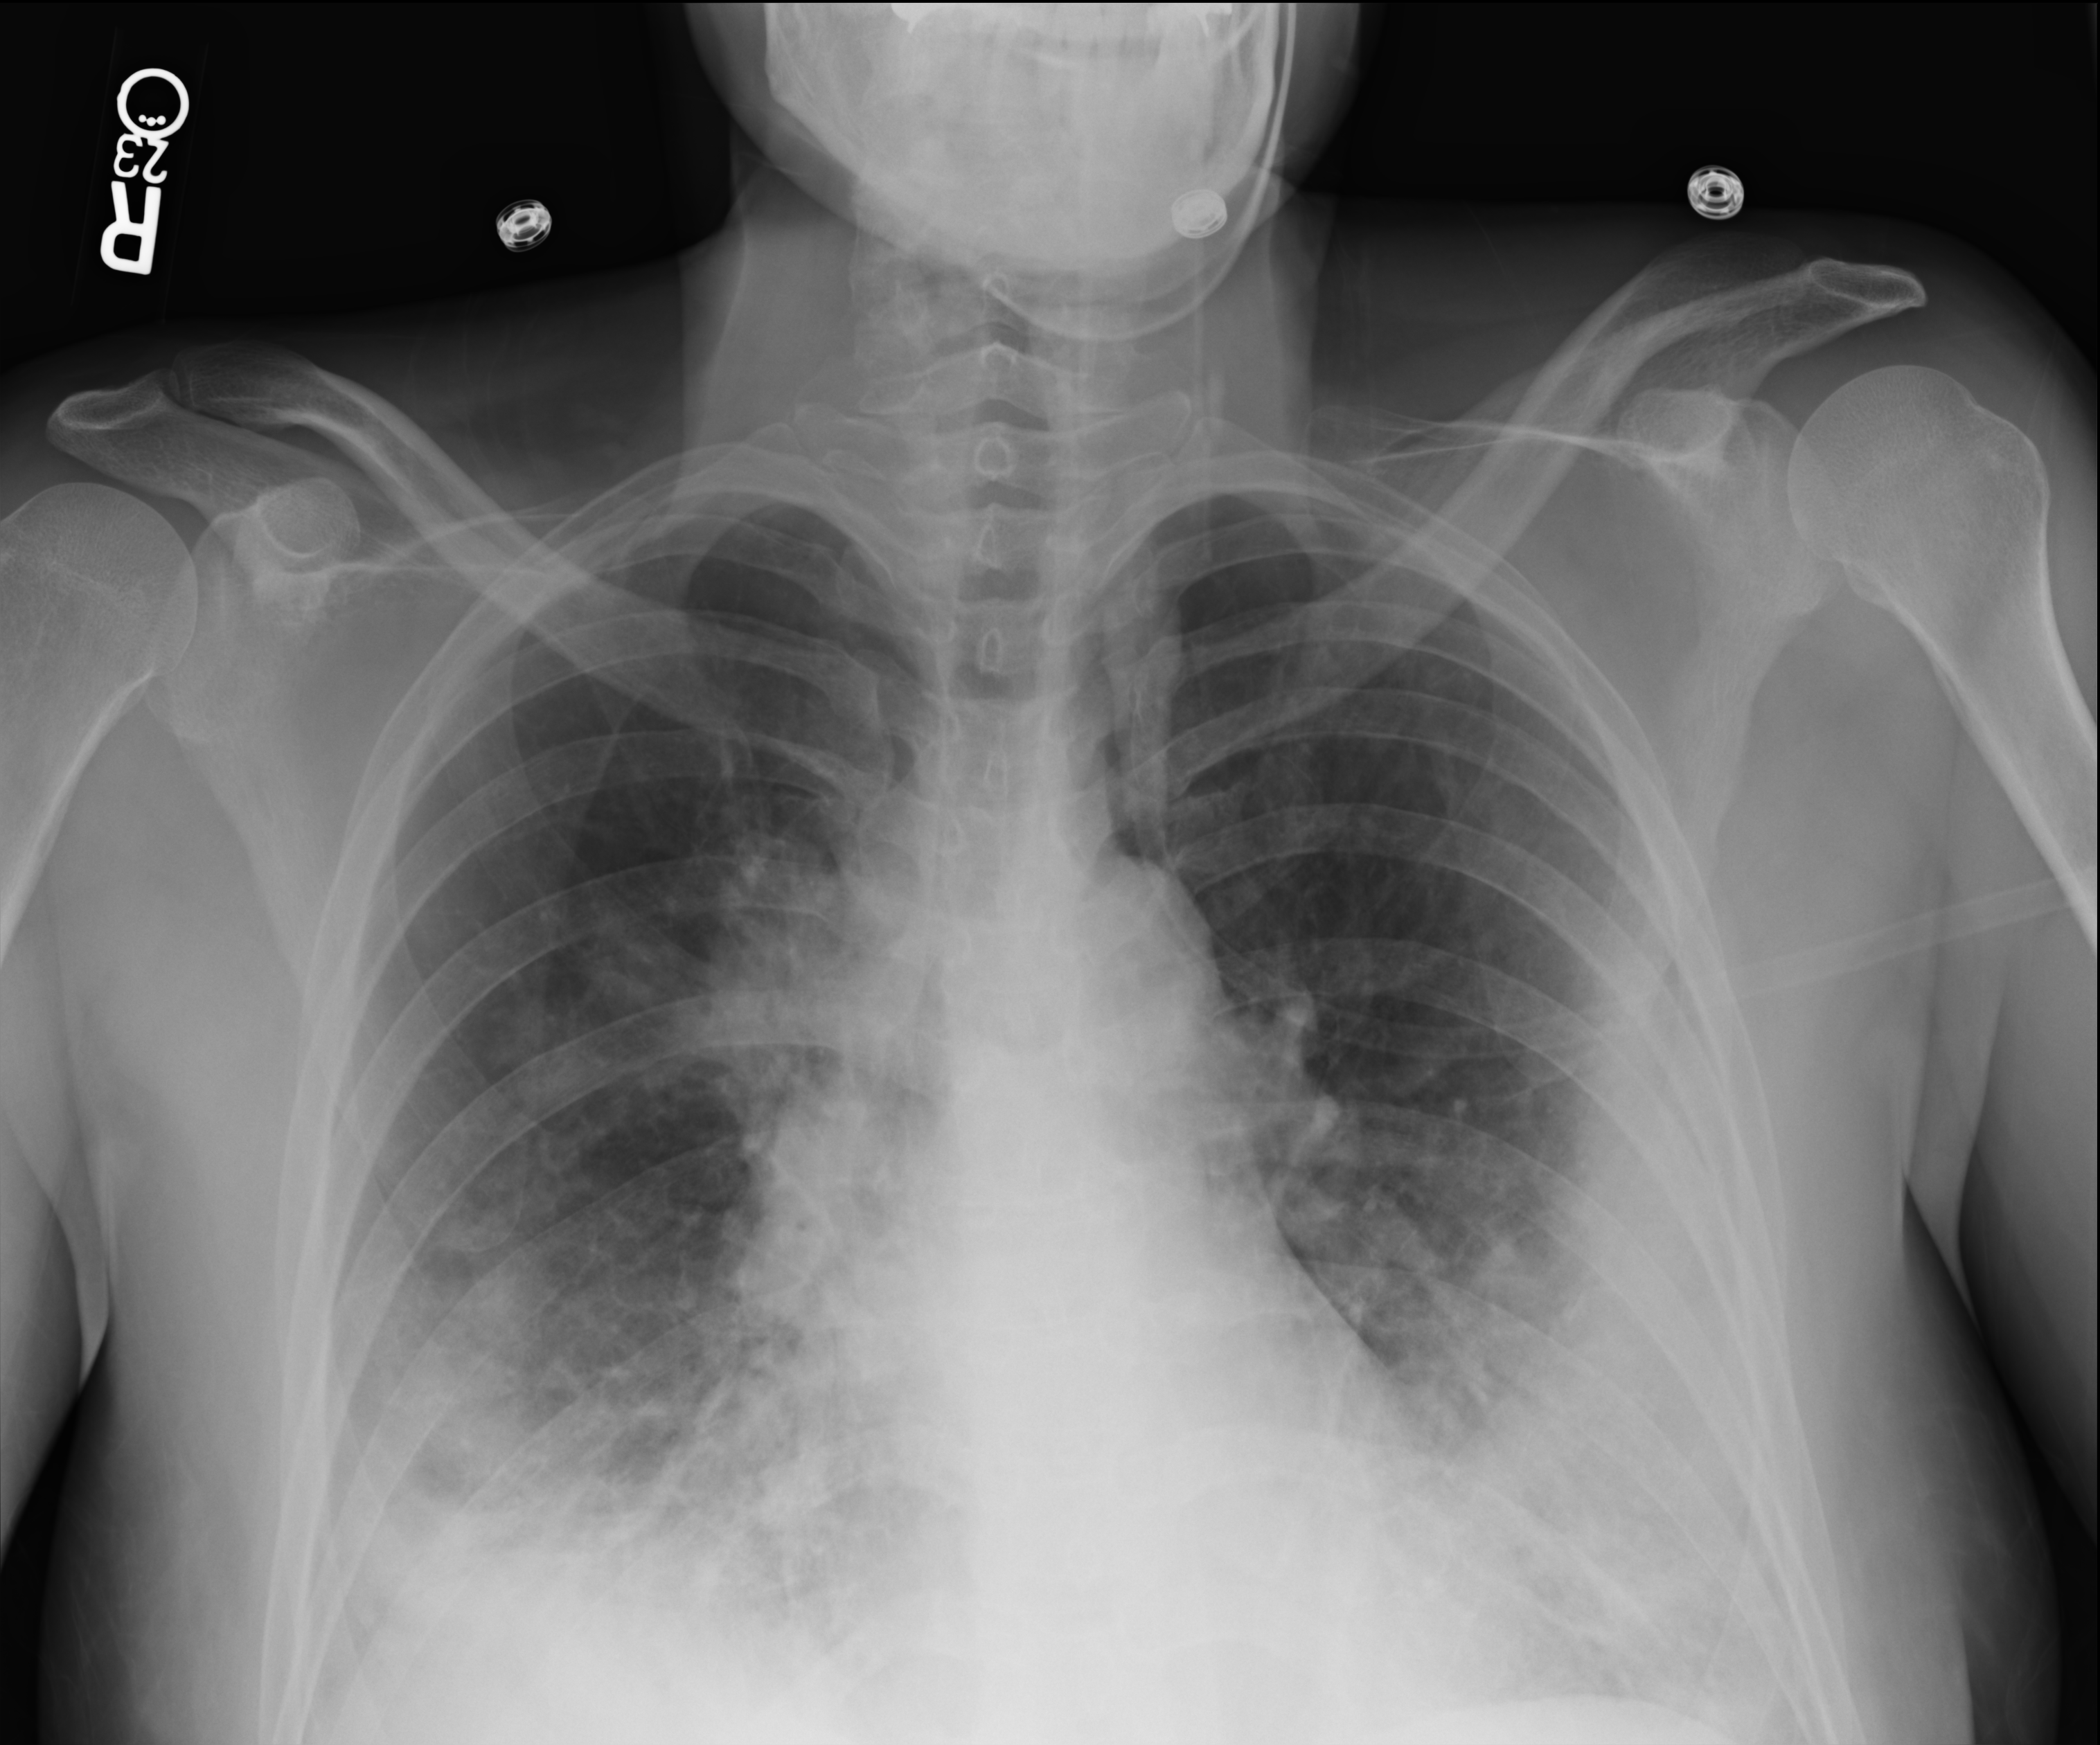
Portable chest radiograph. Patient hospitalised with COVID-19; female, aged 18–59 years.
From the hospital-stay record, not from the radiograph (when in the stay this image was taken is not recorded): admitted to intensive care during this hospital stay: yes; mechanically ventilated during this hospital stay: no.